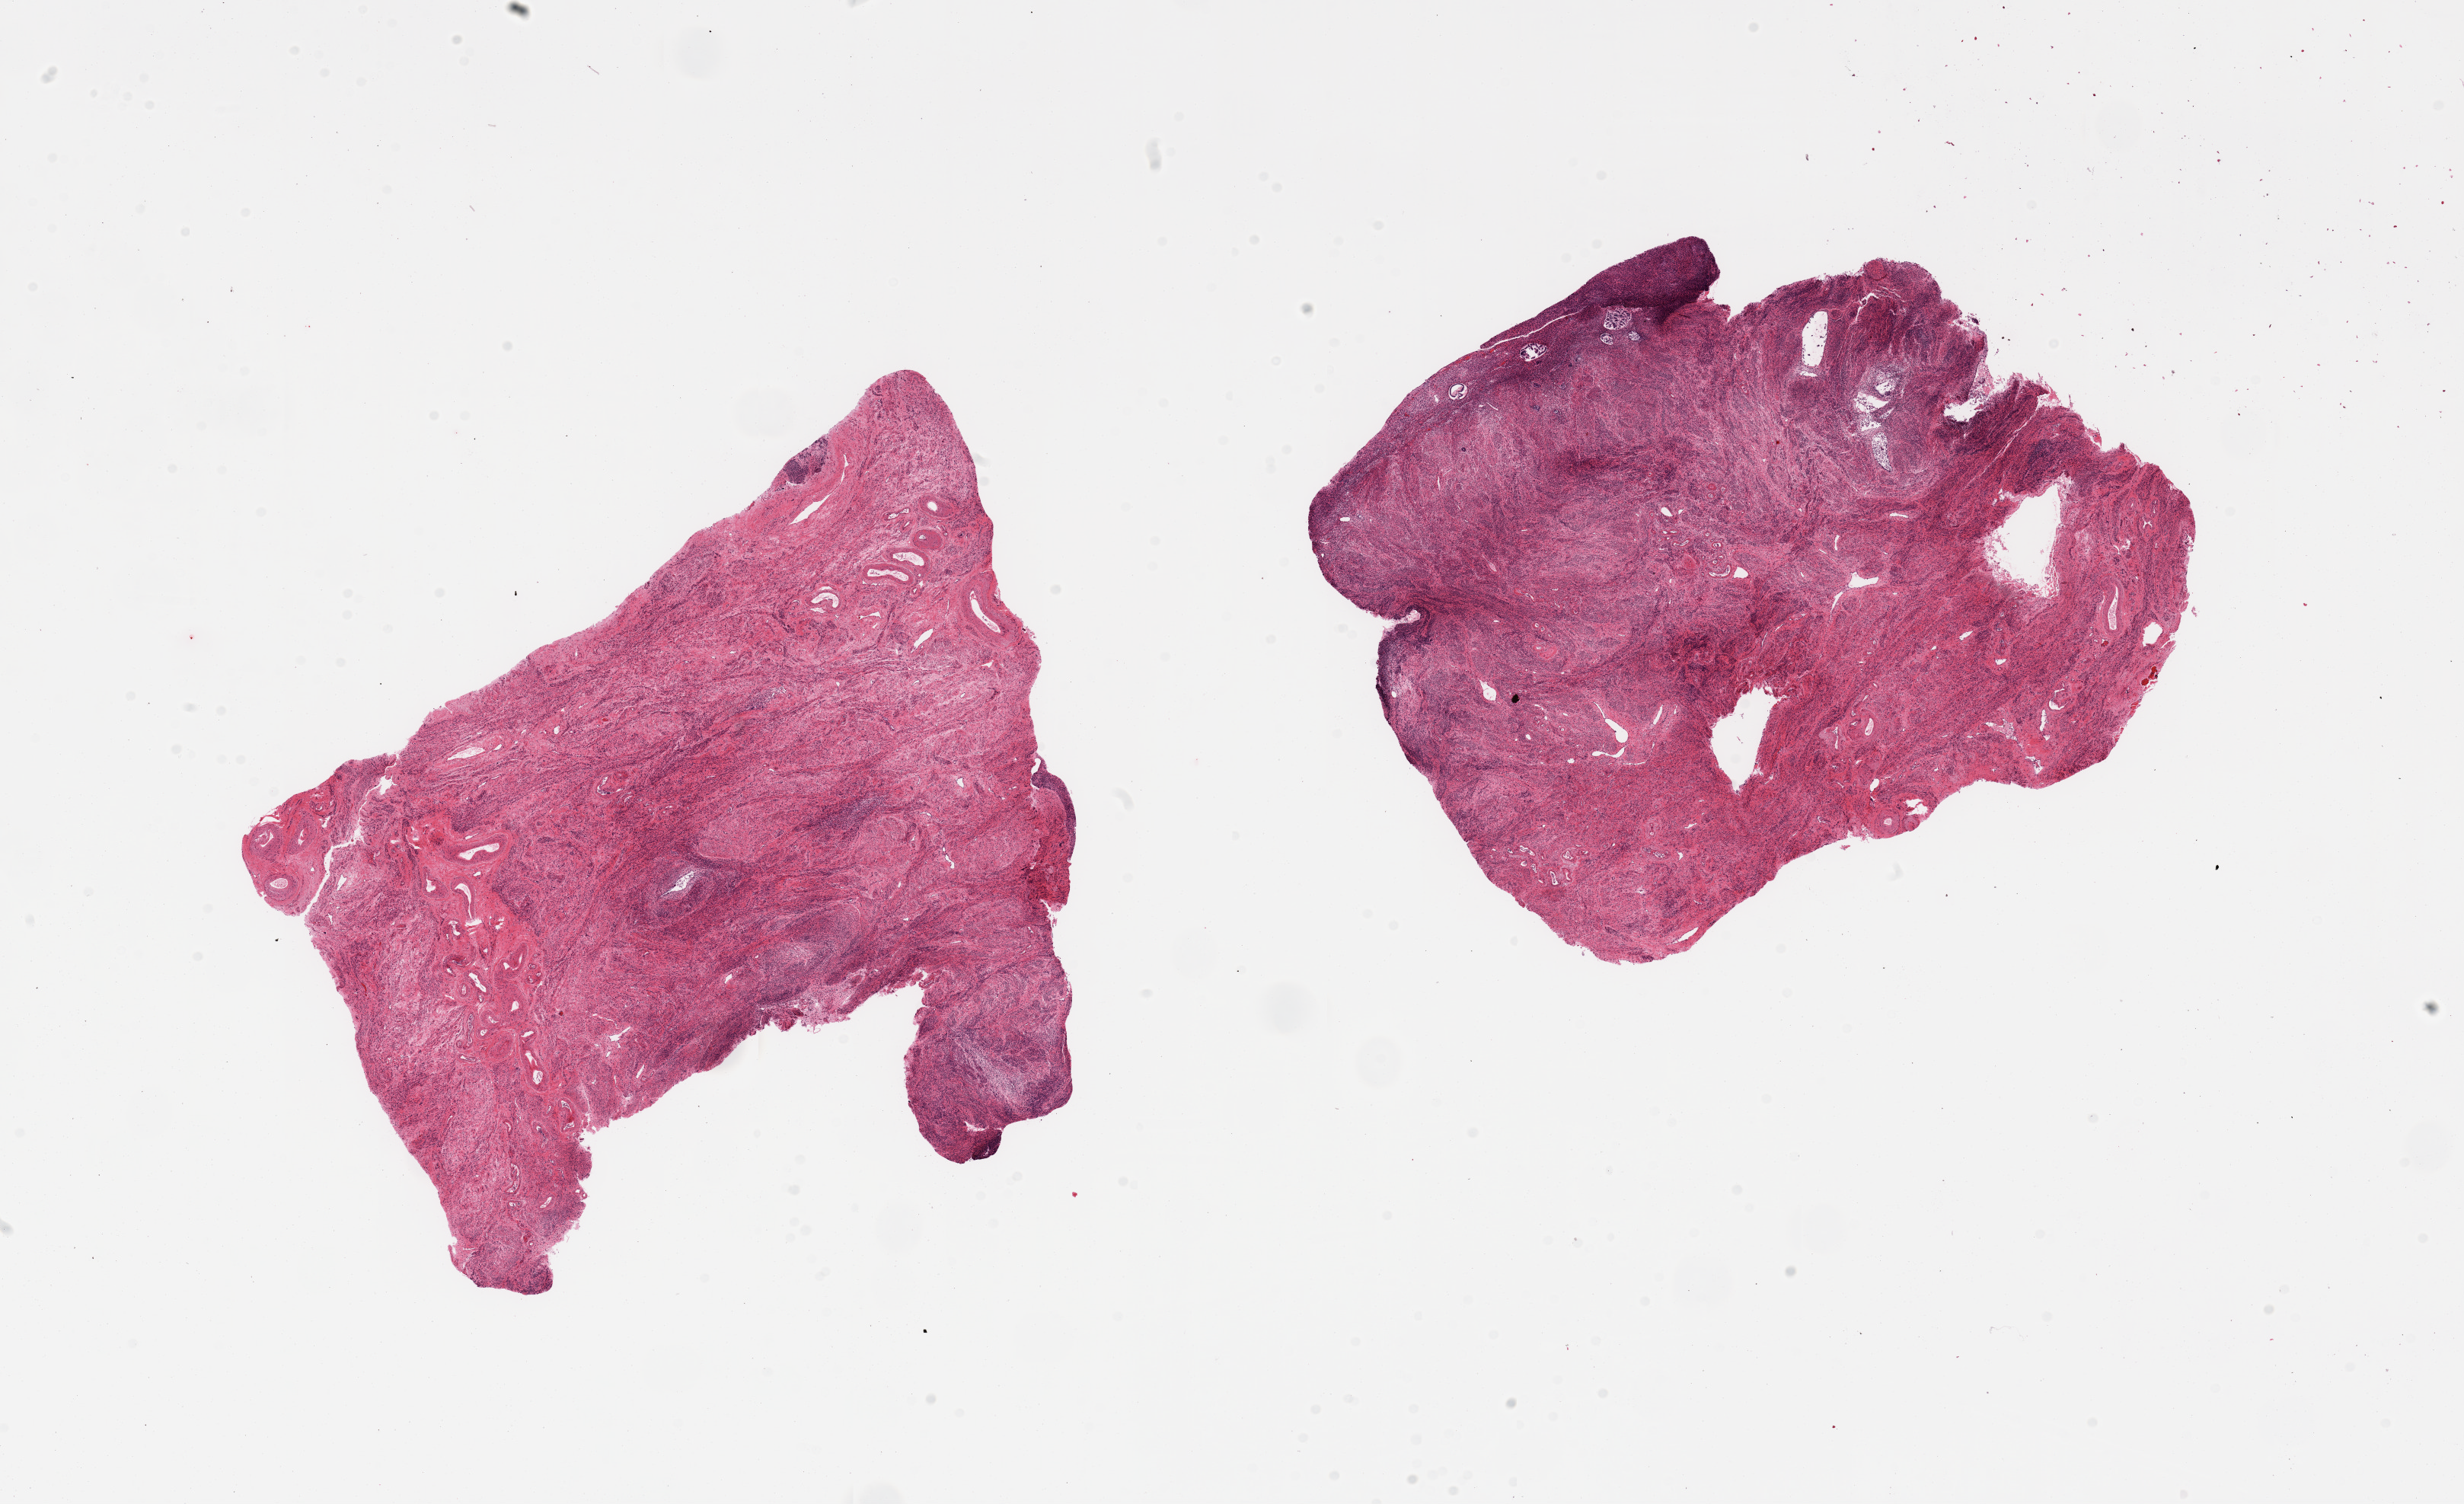
Digitized haematoxylin and eosin-stained section, whole scanned area (about 25.6 x 15.6 mm, slide scanned at 20x) shown as a low-resolution overview. PAXgene-fixed, paraffin-embedded tissue. Target tissue: uterus. Tissue donor sample.
Pathologist's review note for this sample: 2 pieces; glands = 3; stroma = 2.